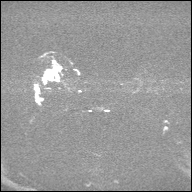
Breast MRI, one axial slice. Position 25 of 32 along the scan axis. Diffusion-weighted series; image 2 of 4 stored at this slice position (different b-values; order by instance number). 1.5 T. 4 mm slice thickness. 192 × 192 image matrix, field of view 360 × 360 mm. Female patient.
Outlined on this slice (outlined manually by an expert reader):
- tumour on diffusion-weighted imaging: bounding box (x1, y1, x2, y2) in pixels: (47, 69, 57, 79)